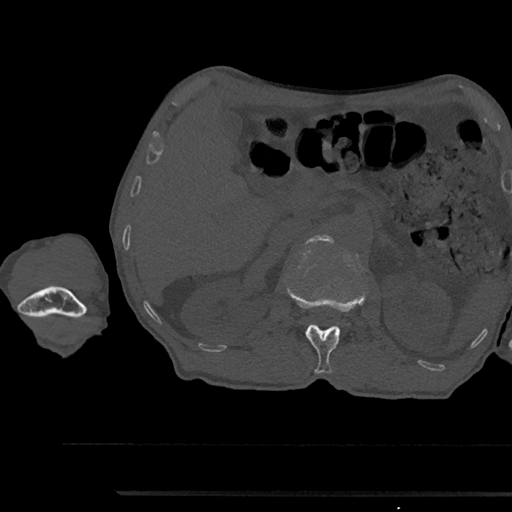
CT including the spine, one axial slice. Position 619 of 797 along the scan axis. Reconstruction kernel Br40s/3. 120 kVp. Bone window (W 1800 / L 400 HU). 0.5 mm slice thickness. 512 × 512 image matrix. Male patient, age 79 years. Case-level facts recorded for this patient, not image findings: primary cancer: prostate.
Annotated regions visible in this slice (semi-automatically segmented with operator editing):
- L1 vertebra: bounding box (x1, y1, x2, y2) in pixels: (288, 288, 365, 374)
- L2 vertebra: (307, 235, 334, 244)